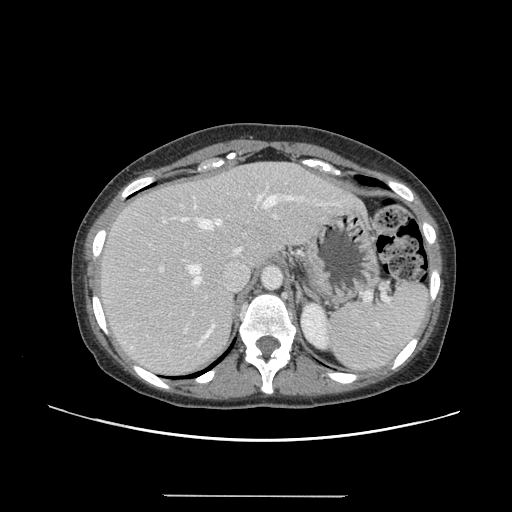
Contrast-enhanced abdominal CT, one axial slice; position 107 of 144 along the scan axis; 120 kVp; intravenous contrast given; soft-tissue window (W 400 / L 40 HU); 512 × 512 image matrix, field of view 380 × 380 mm. Female patient, age 53 years. Case-level facts recorded for this patient, not image findings: diagnosis: colorectal cancer liver metastases, imaged before liver resection; multiple liver metastases: yes; largest metastasis: 1.1 cm; disease in both lobes: no.
Structures marked on this image (outlined manually by an expert reader):
- hepatic veins: bounding box (x1, y1, x2, y2) in pixels: (182, 195, 292, 284)
- liver: (99, 162, 360, 375)
- planned liver remnant (the part of the liver to remain after resection): (92, 162, 298, 301)
- portal vein (with intrahepatic branches): (159, 215, 277, 315)